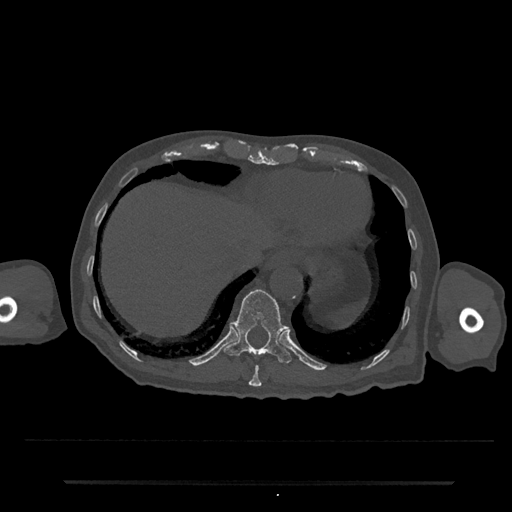
CT including the spine, one axial slice; slice 266 of 797 in the series (ordered by position); reconstruction kernel Br40s/3; 120 kVp; bone window (W 1800 / L 400 HU); 0.5 mm slice thickness; 512 × 512 image matrix, field of view 427 × 427 mm. Male patient, age 74 years. Case-level facts recorded for this patient, not image findings: primary cancer: prostate.
Structures marked on this image (semi-automatic segmentation, software-assisted and operator-edited):
- T10 vertebra: box from (x=249, y=365) to (x=262, y=387) px
- T11 vertebra: (x=224, y=289)–(x=292, y=364)